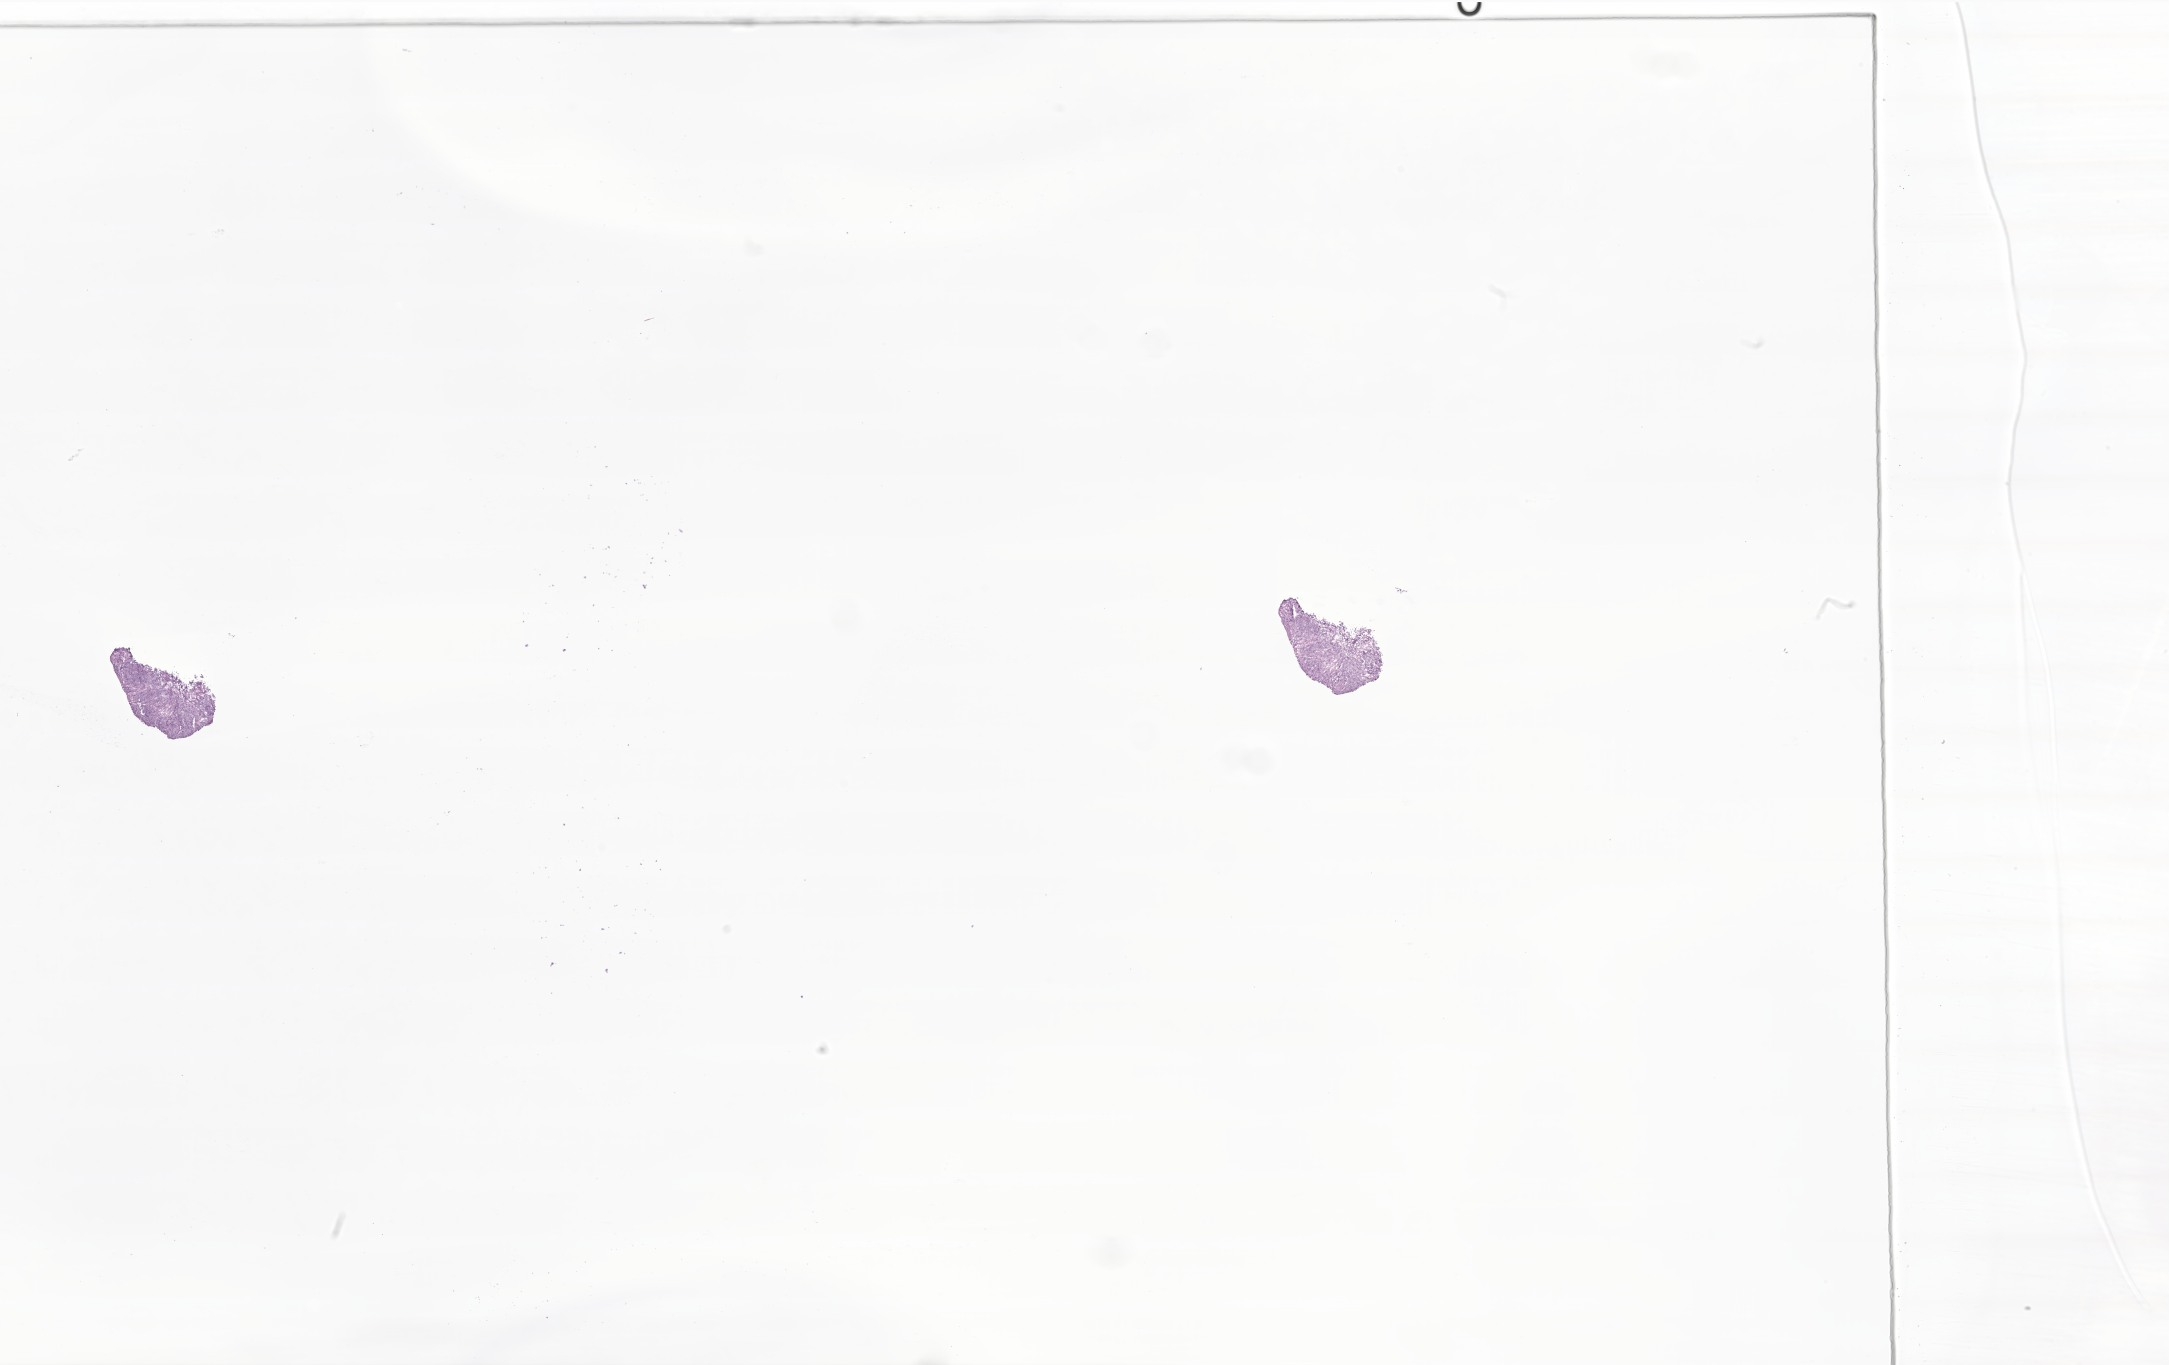
Haematoxylin and eosin whole-slide image of tumor tissue from the soft tissue of lower extremity, whole scanned area (about 36.6 x 23.0 mm) shown as a low-resolution overview; frozen section. Patient male; age 58 months.
Tissue or organ of origin (case record): connective, subcutaneous and other soft tissues of lower limb and hip. Diagnosis: Undifferentiated sarcoma.